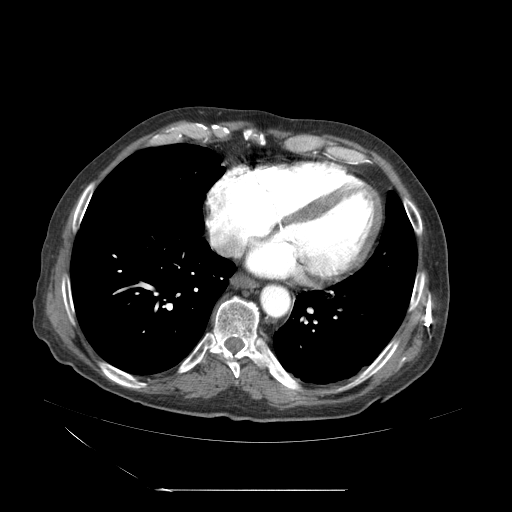
Contrast-enhanced abdominal CT (liver protocol), one axial slice; slice 65 of 71 in the series (ordered by position); soft-tissue window (W 400 / L 40 HU); 512 × 512 image matrix, field of view 440 × 440 mm. Case-level facts recorded for this patient, not image findings: diagnosis: hepatocellular carcinoma (patient treated with transarterial chemoembolisation; whether this scan precedes or follows treatment is not stated here); TNM stage (as recorded): Stage-II; Child-Pugh class: A; tumour nodularity: multinodular; tumour size: 1 cm.
Structures marked on this image (semi-automatic segmentation, software-assisted and operator-edited):
- abdominal aorta: bounding box (x1, y1, x2, y2) in pixels: (260, 284, 289, 318)